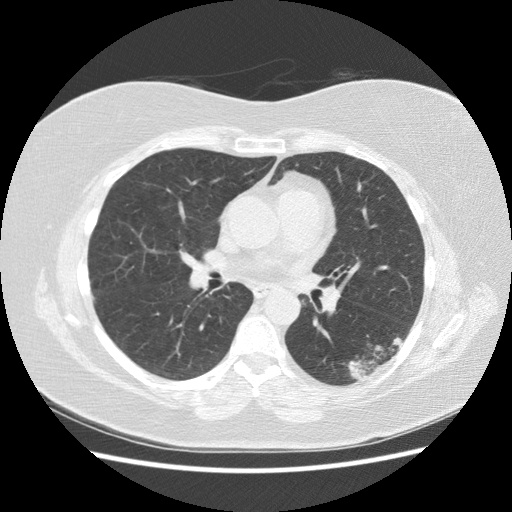
Axial slice from a low-dose chest CT screening exam, third annual screen, lung window (W 1500 / L -600 HU), 2.5 mm slice thickness, standard (soft-tissue) reconstruction kernel (STANDARD), 120 kVp, slice 83 of 151 in the series. Female, age 57 years at enrolment. Current smoker at enrolment.
Expert reader's lesion annotation, box from (x=332, y=325) to (x=410, y=387) px. Reader record for this screening exam (exam-level; its link to the box is not recorded): non-calcified nodule or mass ≥4 mm, left lower lobe, 40 × 20 mm, poorly defined margins, mixed attenuation, pre-existing on the prior screen: yes; interval growth: yes. Participant outcome: lung cancer diagnosed 55 days after this screen — squamous cell carcinoma, NOS, left lower lobe, poorly differentiated (G3), stage IB (AJCC 6th edition), 40 mm at pathology.